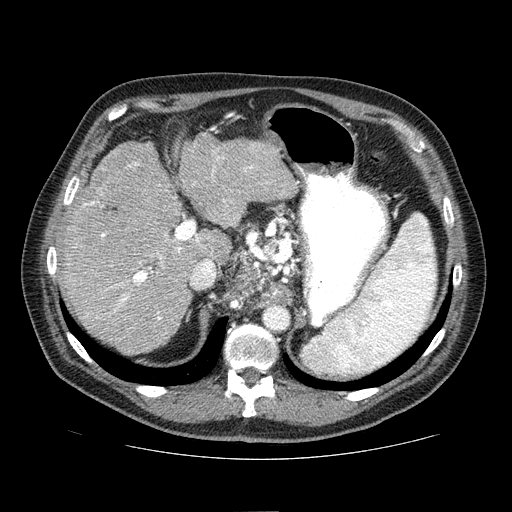
Contrast-enhanced abdominal CT (liver protocol), one axial slice; position 49 of 81 along the scan axis; reconstruction kernel STANDARD; one of 2 acquisitions stored at this slice position; soft-tissue window (W 400 / L 40 HU); 2.5 mm slice thickness; 512 × 512 image matrix. From the clinical record (not read from this slice): diagnosis: hepatocellular carcinoma (patient treated with transarterial chemoembolisation; whether this scan precedes or follows treatment is not stated here); TNM stage (as recorded): Stage-IIIA; Child-Pugh class: A; tumour differentiation: well differentiated; tumour nodularity: multinodular.
Outlined on this slice (semi-automatically segmented with operator editing):
- liver parenchyma outside the tumour (the mass and vessels are separate outlines, so this box may not span the whole liver): box from (x=60, y=132) to (x=297, y=354) px
- mass: (x=247, y=141)–(x=278, y=170)
- liver vessels: (x=68, y=149)–(x=269, y=320)